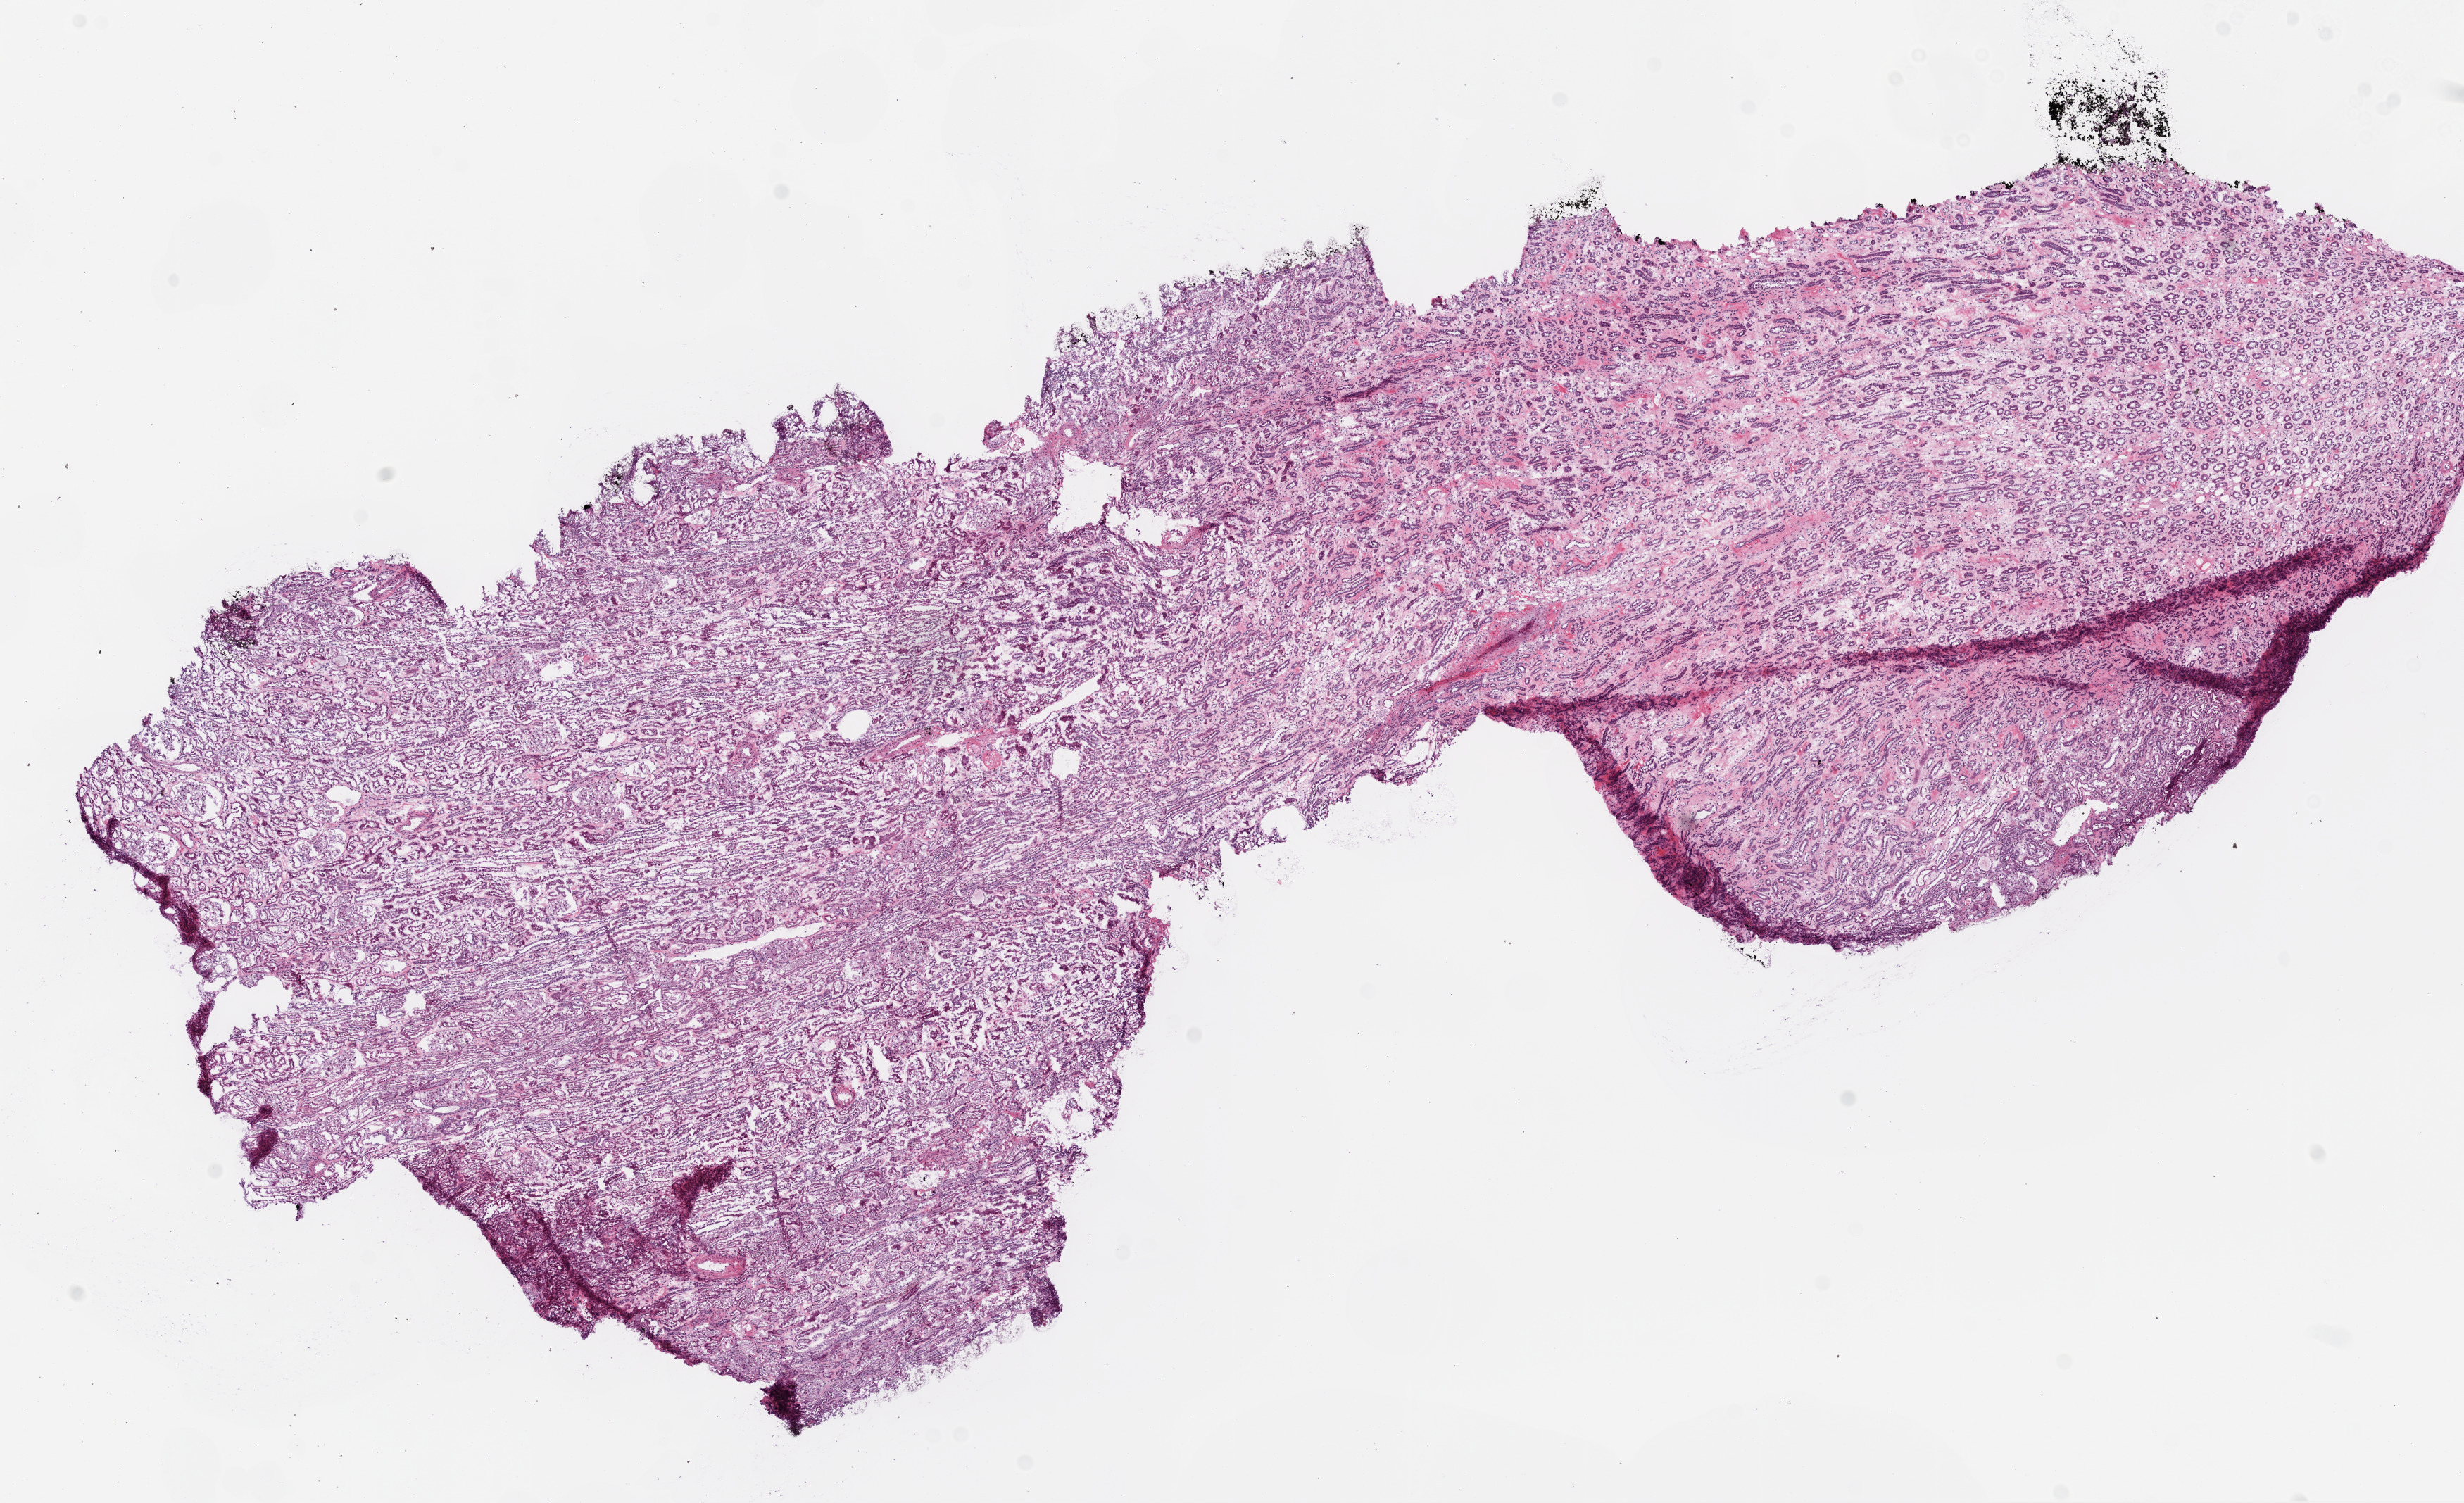
Hematoxylin and eosin (H&E) stained whole-slide image, low-resolution overview of the scanned area, about 14.0 x 8.6 mm, frozen section from the top of the tissue portion, kidney, solid tissue normal (non-tumour tissue) sample. Male, age 75 years at initial diagnosis.
This section: solid tissue normal (non-tumour) sample from the same patient. Patient diagnosis: Clear cell adenocarcinoma, NOS.